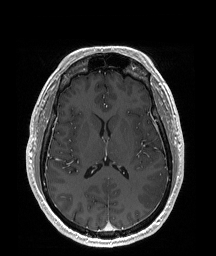
Brain MRI from a brain-tumour surgery series, one axial slice; position 92 of 192 along the scan axis; T1-weighted post-contrast; 1 mm slice thickness; 216 × 256 image matrix. From the clinical record (not read from this slice): histopathology: Glioblastoma; WHO grade: 4; IDH mutation: no.
Annotated regions visible in this slice (manually delineated by an expert):
- tumour: bounding box <138,173,168,210> (left, top, right, bottom; pixels)